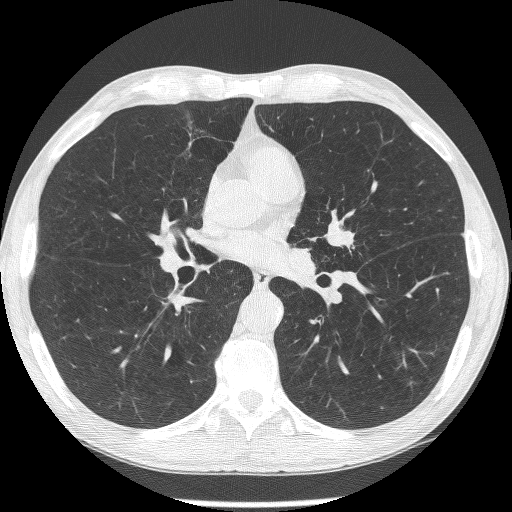
Chest CT (low-dose screening protocol), one axial image, second annual screen, lung window (W 1500 / L -600 HU), 1.25 mm slice thickness, 512 × 512 image matrix. Male, age 62 years at enrolment. Former smoker at enrolment.
• Lesion marked by an expert reader, box from (x=319, y=217) to (x=368, y=265) px.
• The screening reader recorded 2 non-calcified nodules or masses ≥4 mm on this exam; which of them this box marks is not recorded.
• Participant outcome: lung cancer diagnosed 95 days after this screen — small cell carcinoma, NOS, left upper lobe, stage IIIA (AJCC 6th edition).